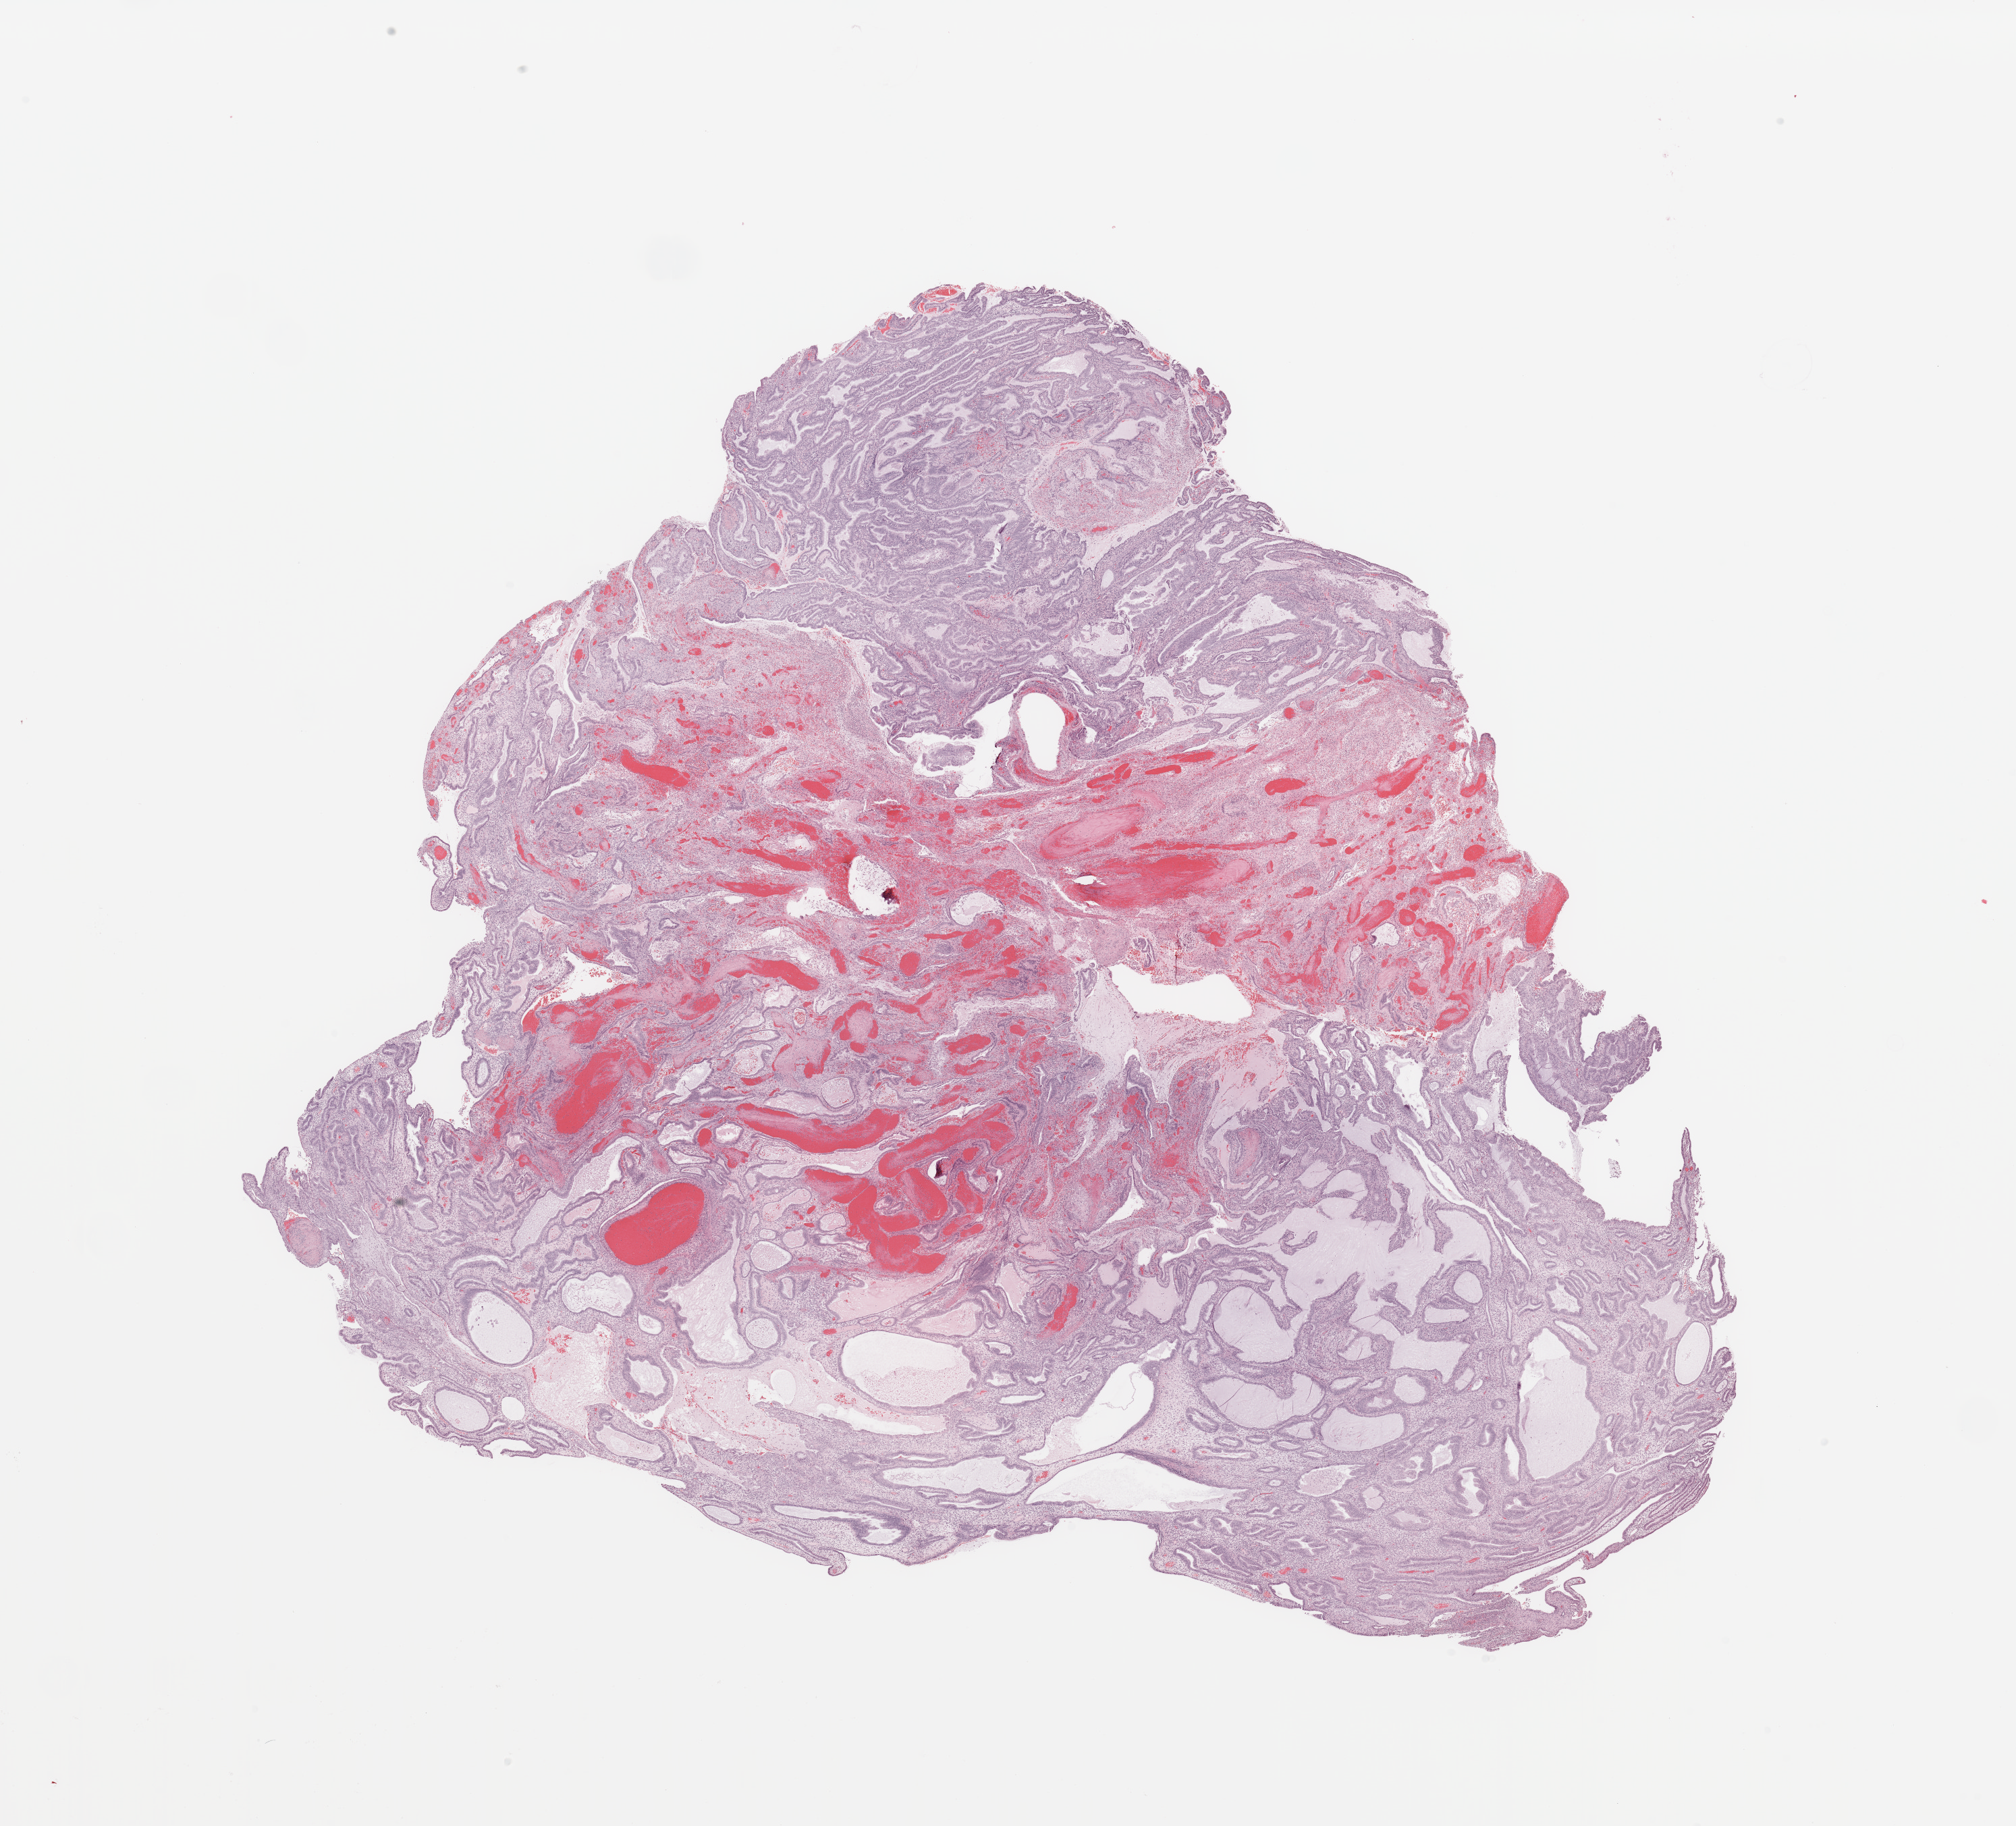
Whole-slide histology image, Hematoxylin and eosin (H&E) stained — whole scanned area (about 23.6 x 21.4 mm, slide scanned at 20x) shown as a low-resolution overview; tumour tissue sample, sampled site: uterus. 58-year-old female patient. Histologic grade: G1 (well differentiated). Pathologist review of this section (percent, as recorded): tumour nuclei 80%, necrosis 0%.
- diagnosis: Endometrioid adenocarcinoma, NOS
- AJCC pathologic stage: I